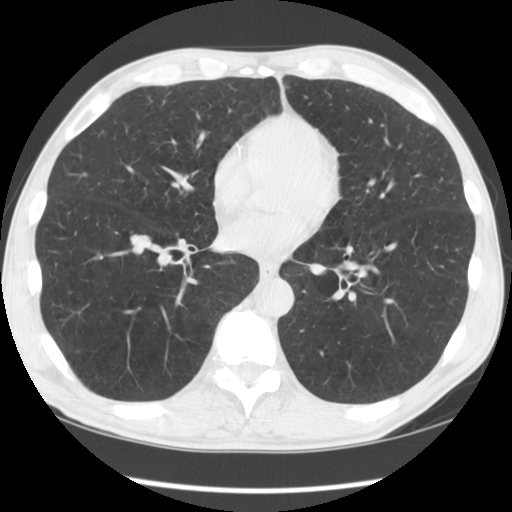
Low-dose screening chest CT, one axial slice; slice 50 of 135 in the series (ordered by position); reconstruction kernel STANDARD; lung window (W 1500 / L -600 HU); 2.5 mm slice thickness; 512 × 512 image matrix.
Structures marked on this image (manually delineated by an expert):
- lesion 1 (tumor, lower lobe of right lung): box from (x=130, y=234) to (x=151, y=254) px